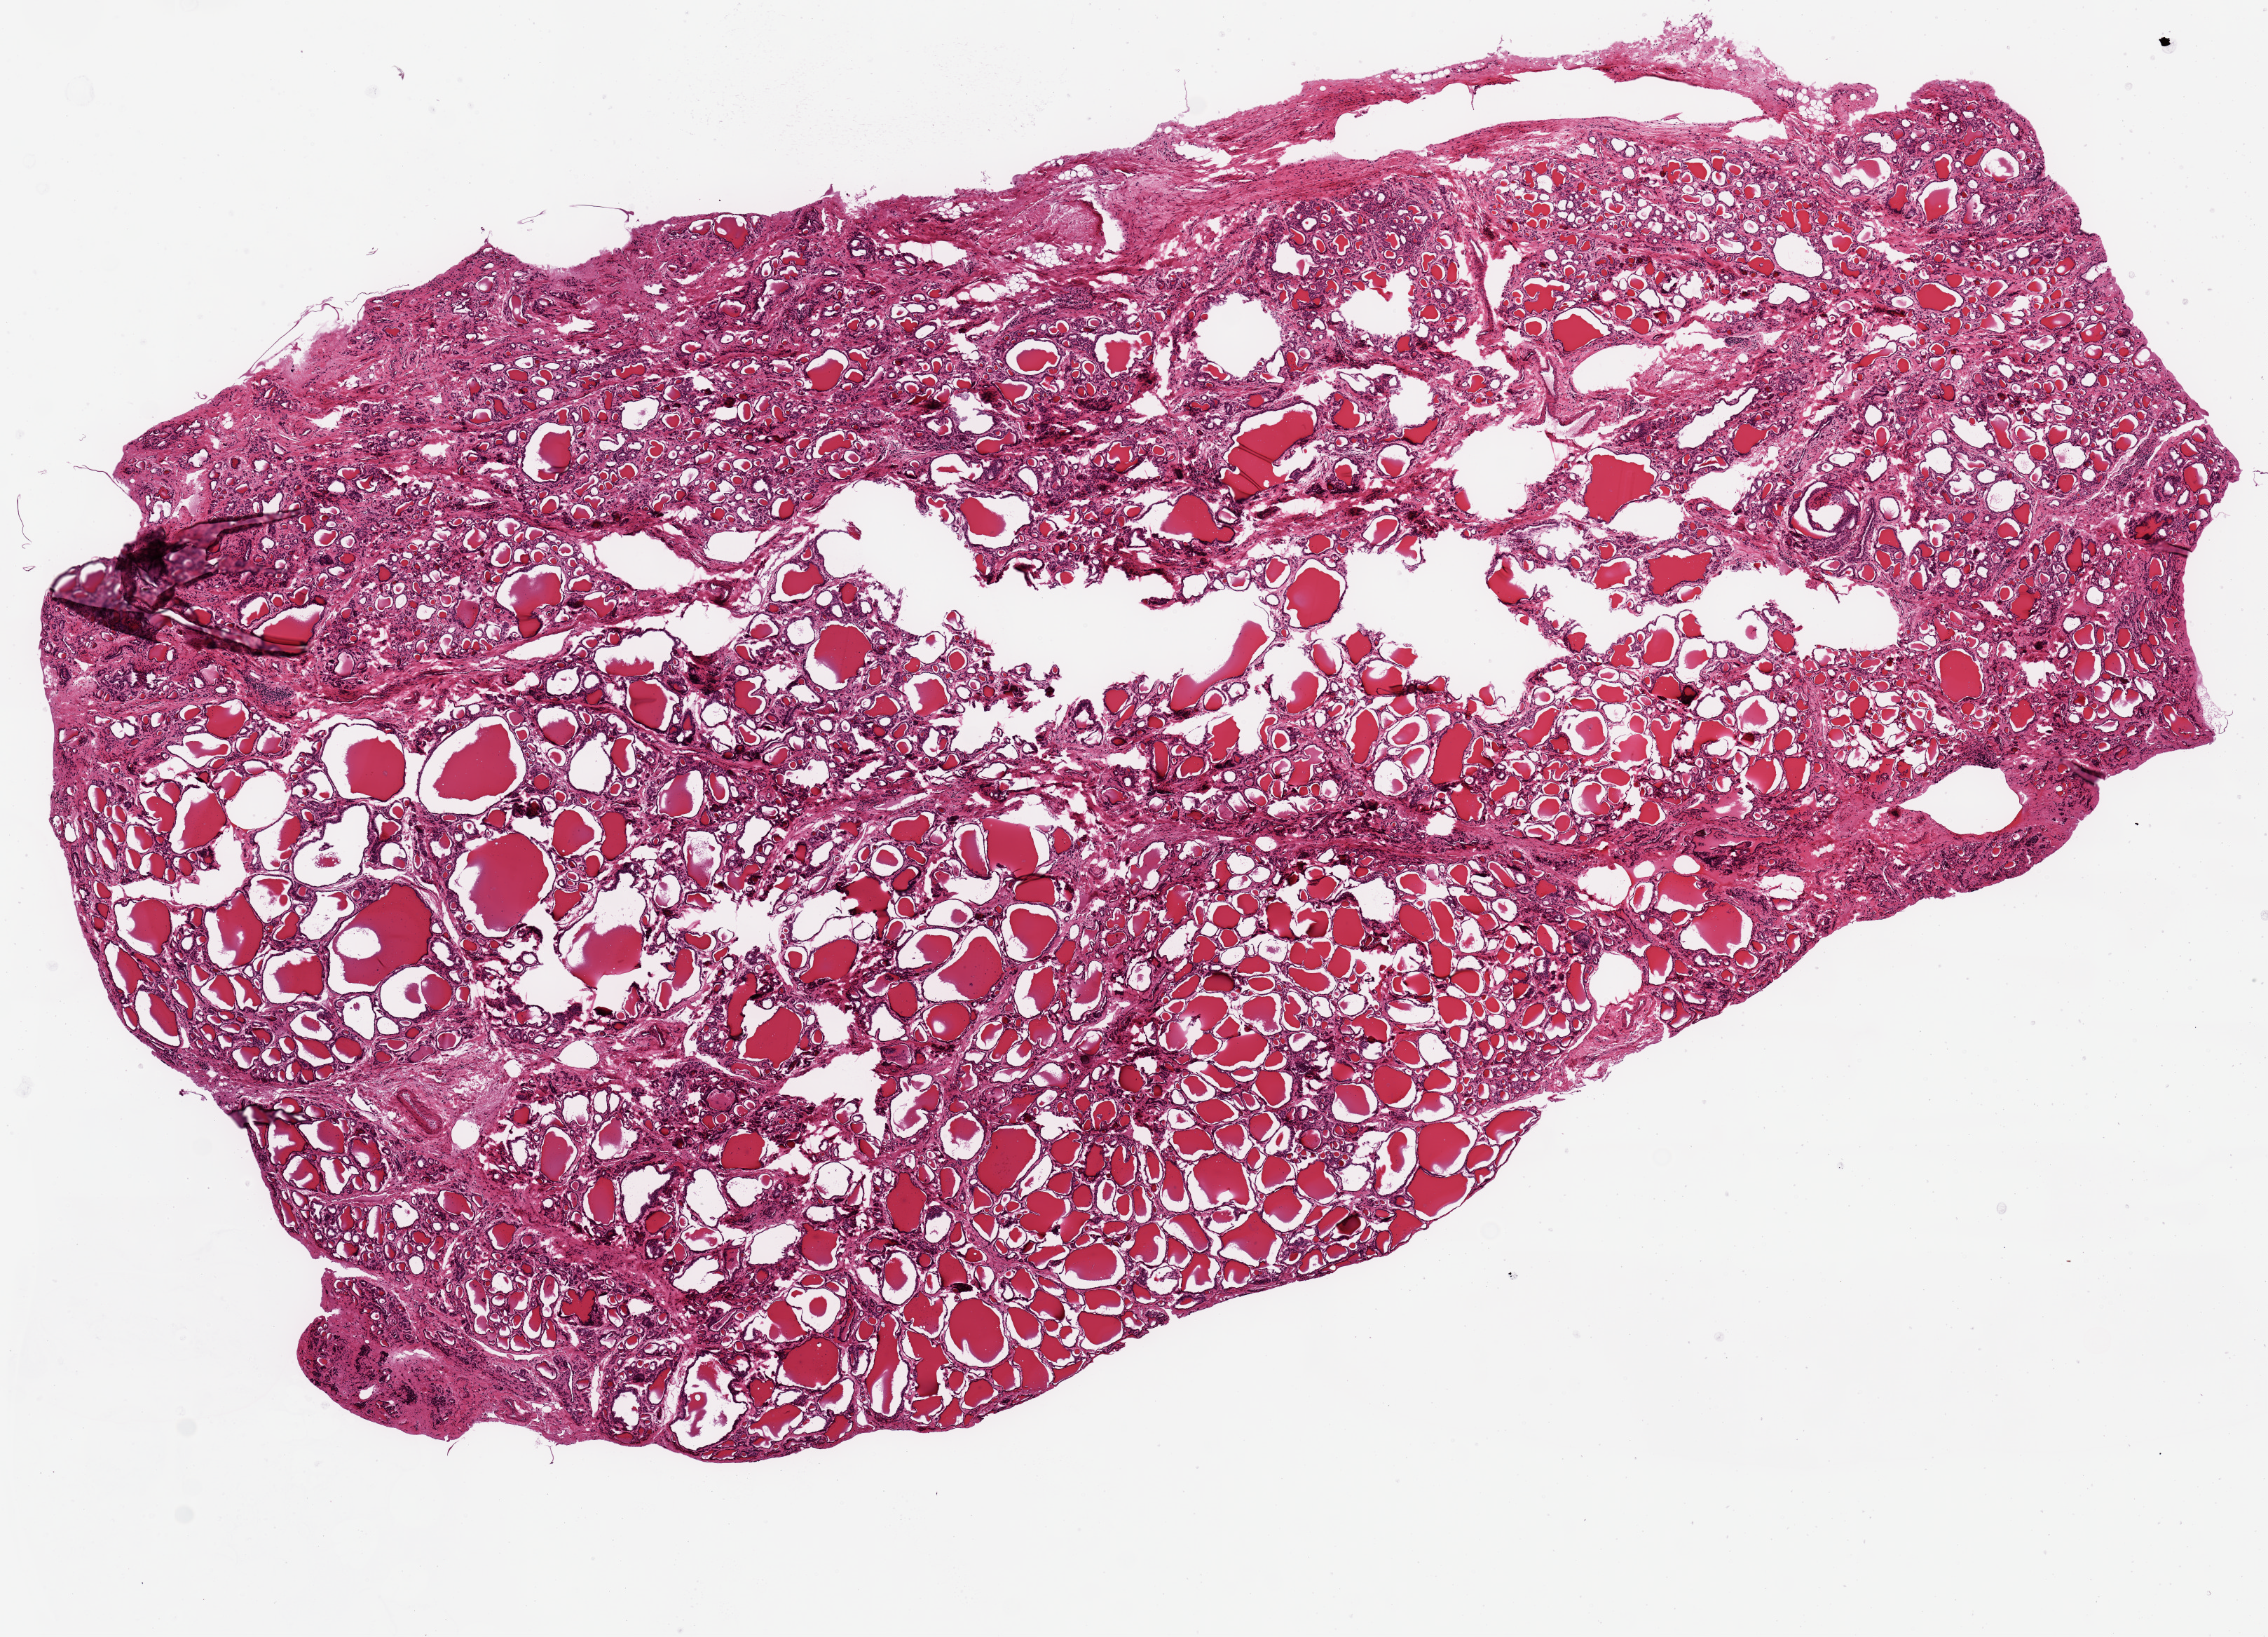
Whole-slide image, H&E stain — a low-resolution overview of the entire scanned area, about 12.8 x 9.2 mm. PAXgene-fixed paraffin-embedded (PFPE) section. Section of thyroid (target tissue). Tissue donor sample. Male donor.
* review note (as recorded): central fracture